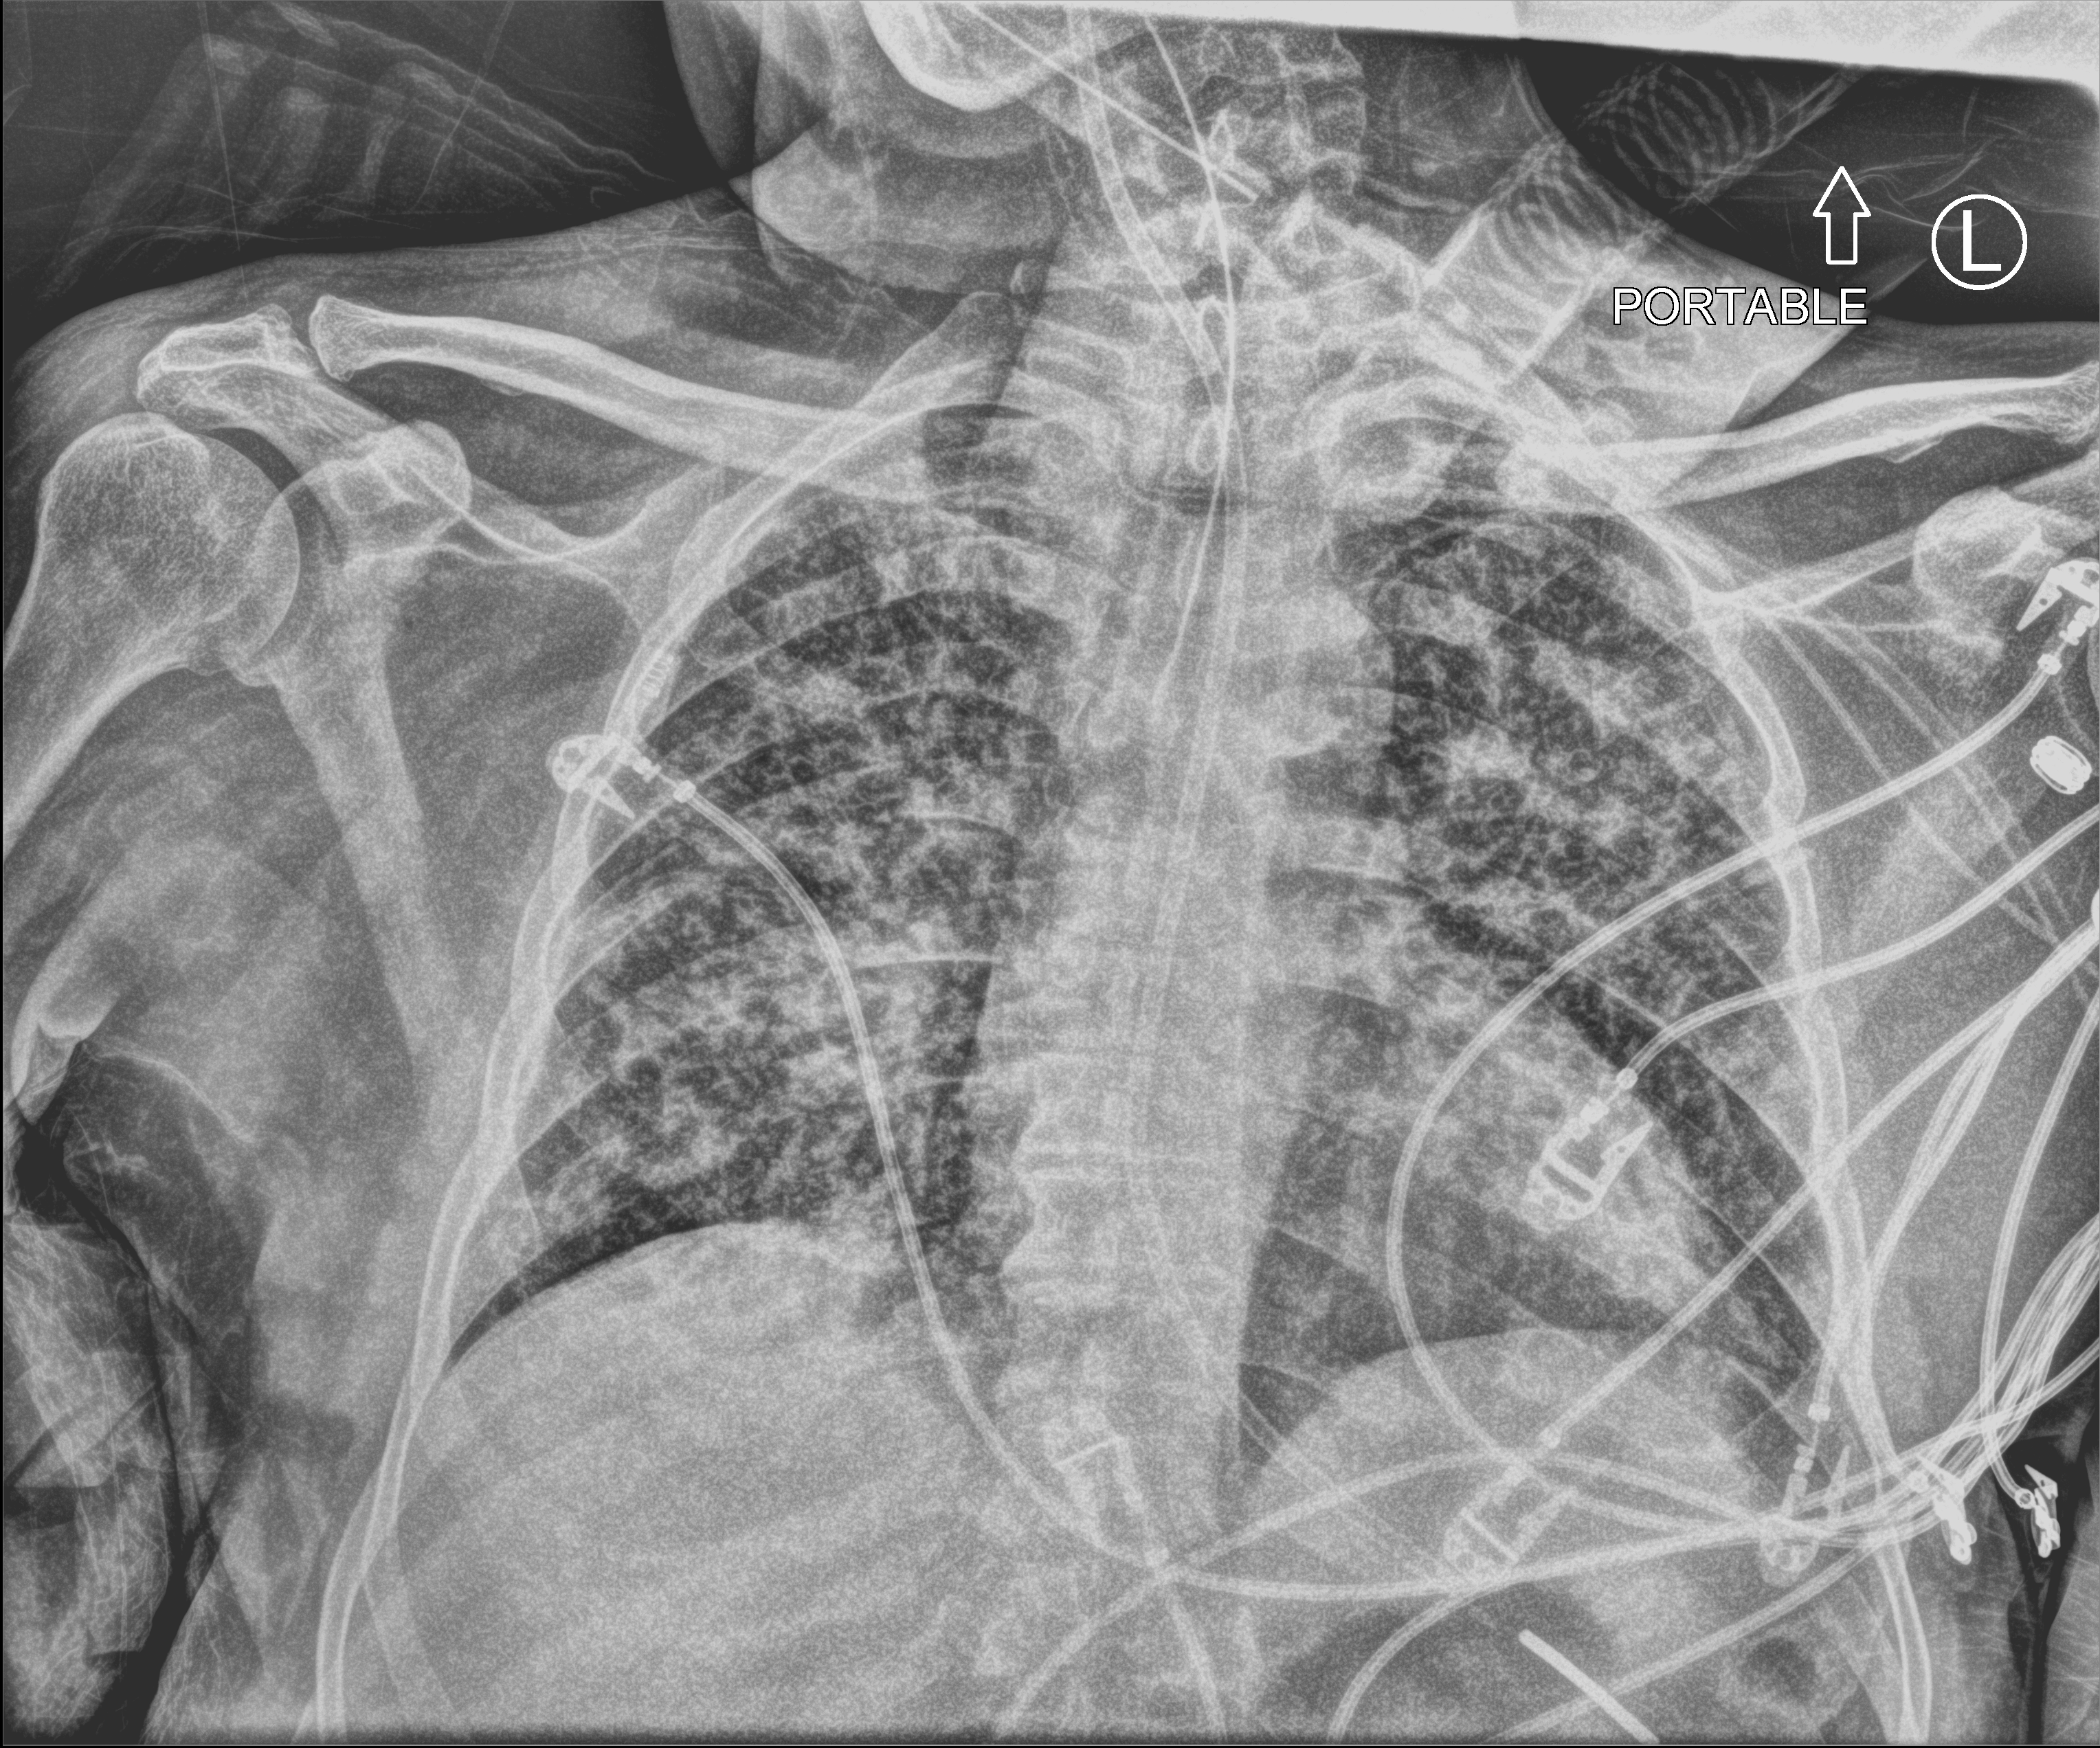
Chest X-ray (portable); anteroposterior (AP) projection. Male patient hospitalised with COVID-19, age 18–59 years.
From the hospital-stay record, not from the radiograph (when in the stay this image was taken is not recorded): COPD (admission record): no.